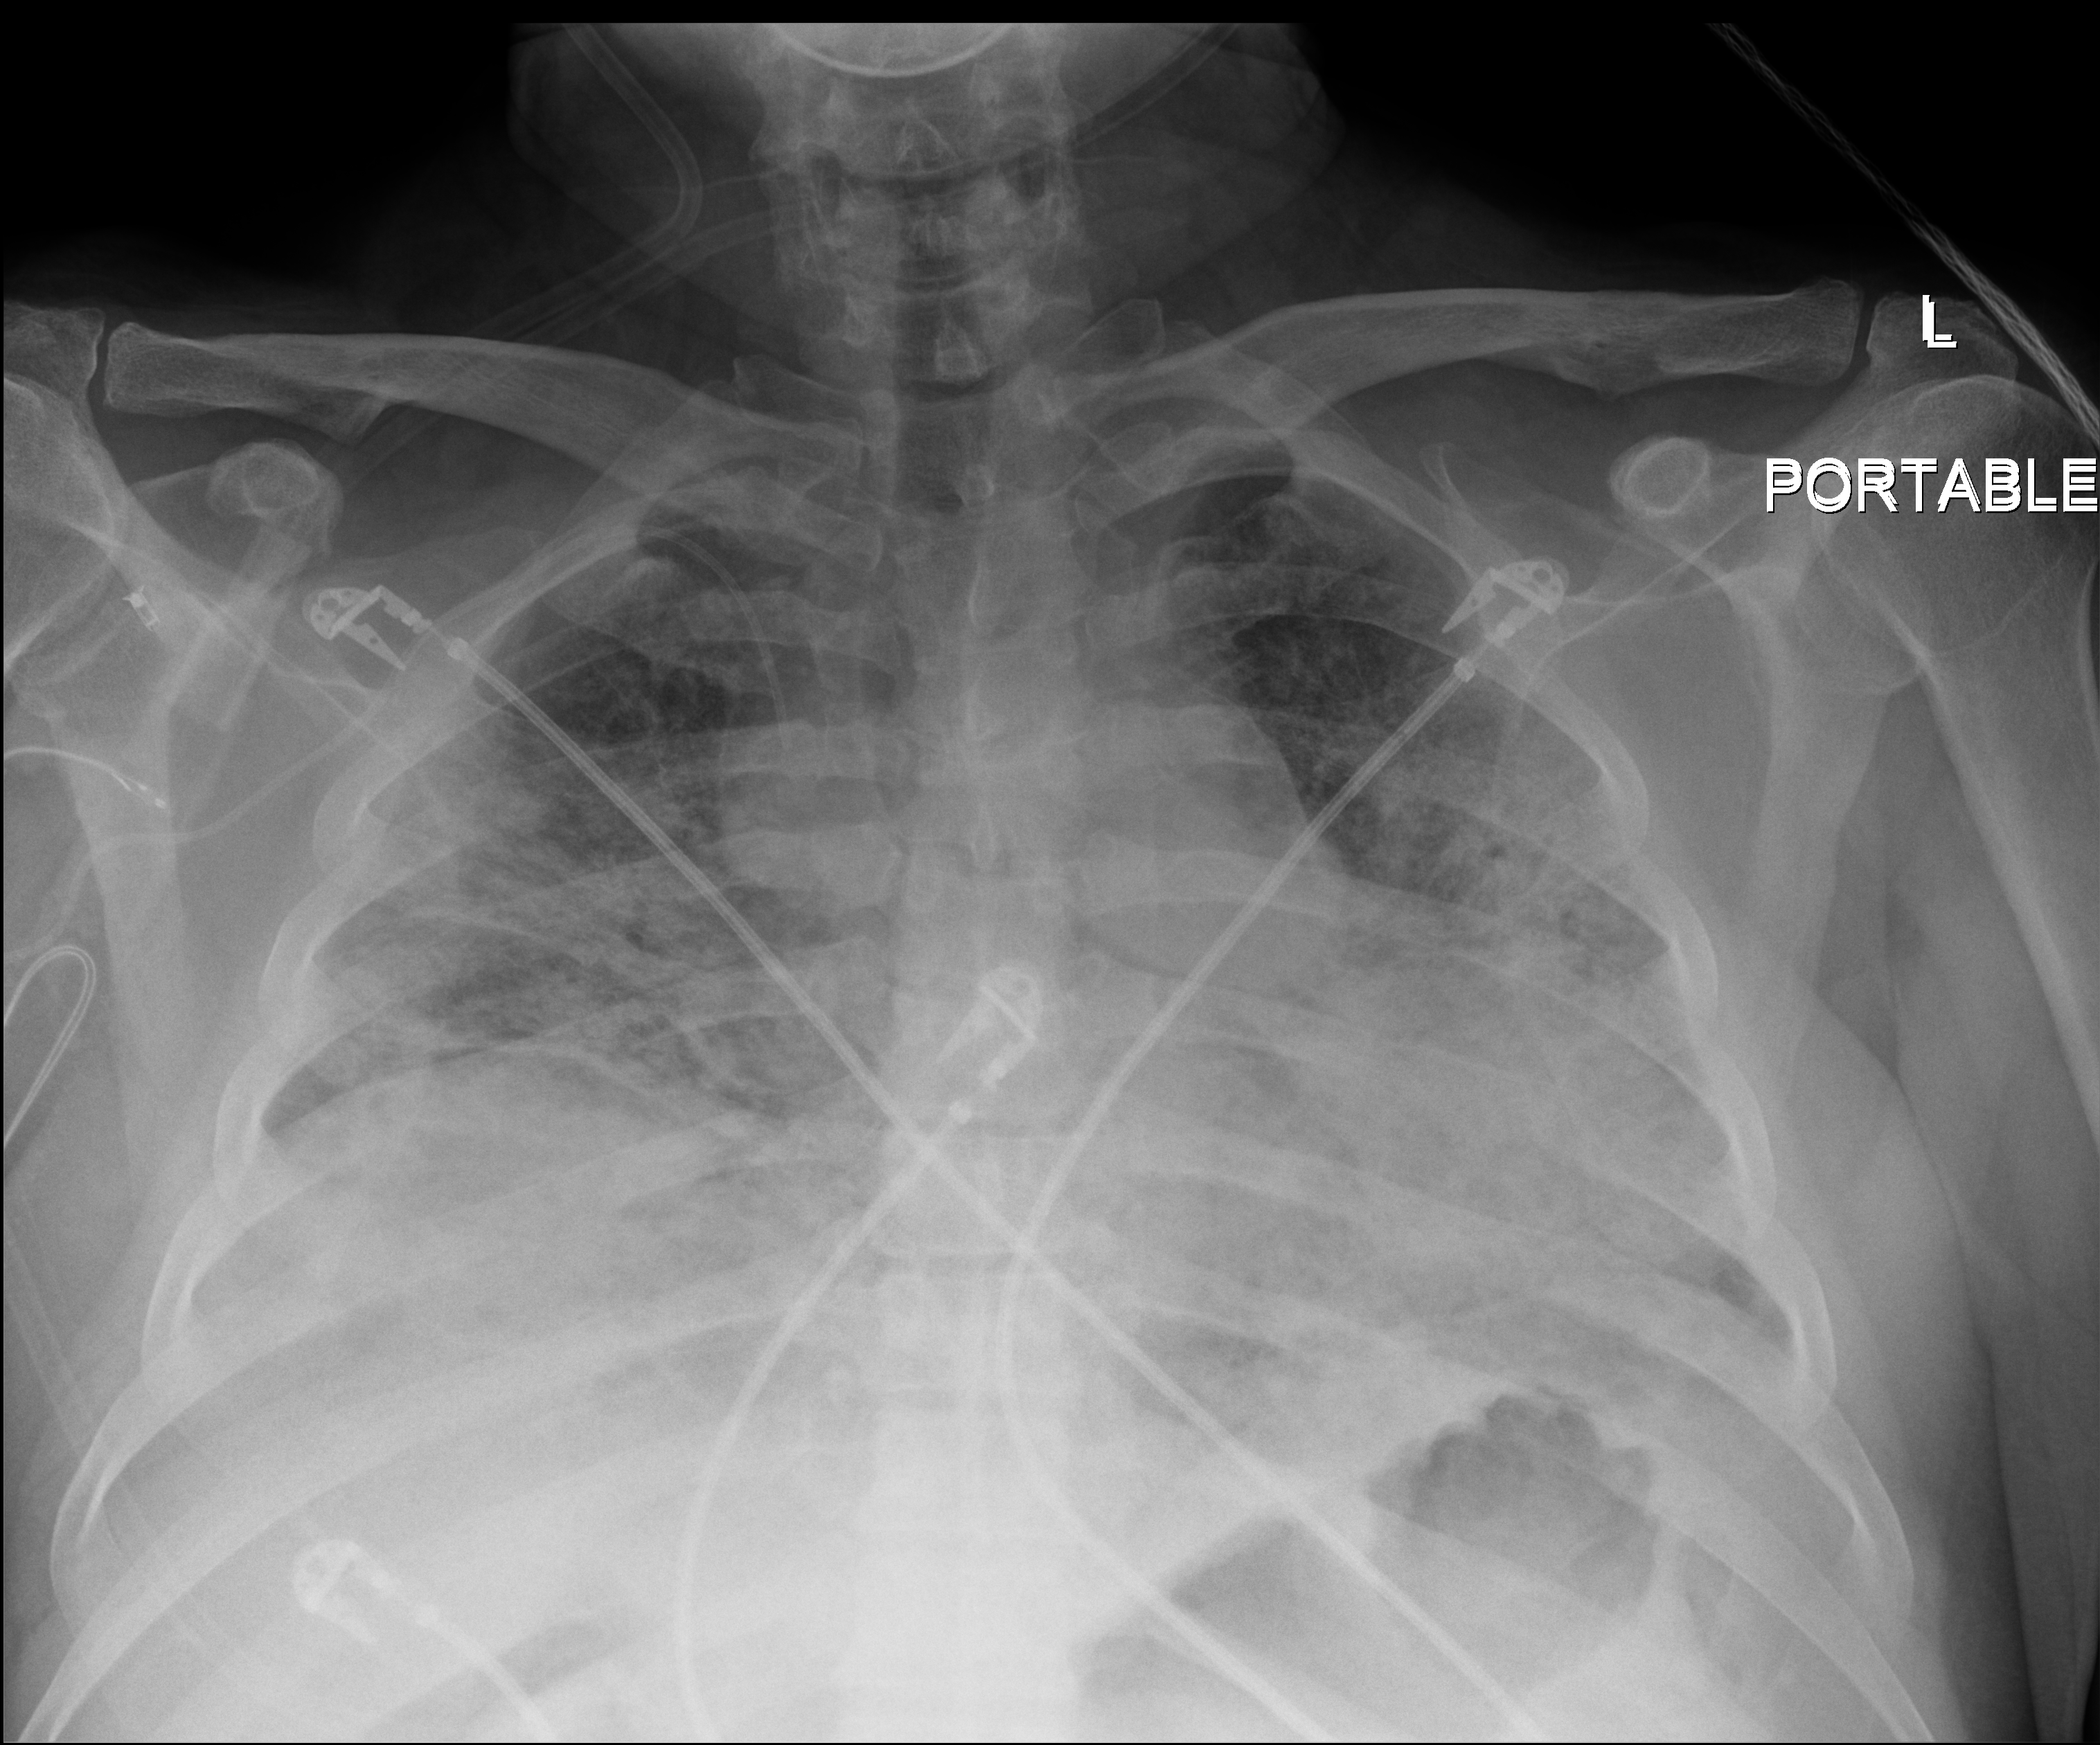
Bedside chest radiograph (digital radiography); anteroposterior (AP) projection. Male patient hospitalised with COVID-19, age 18–59 years.
From the hospital-stay record, not from the radiograph (when in the stay this image was taken is not recorded): admitted to intensive care during this hospital stay: yes; COPD (admission record): no.